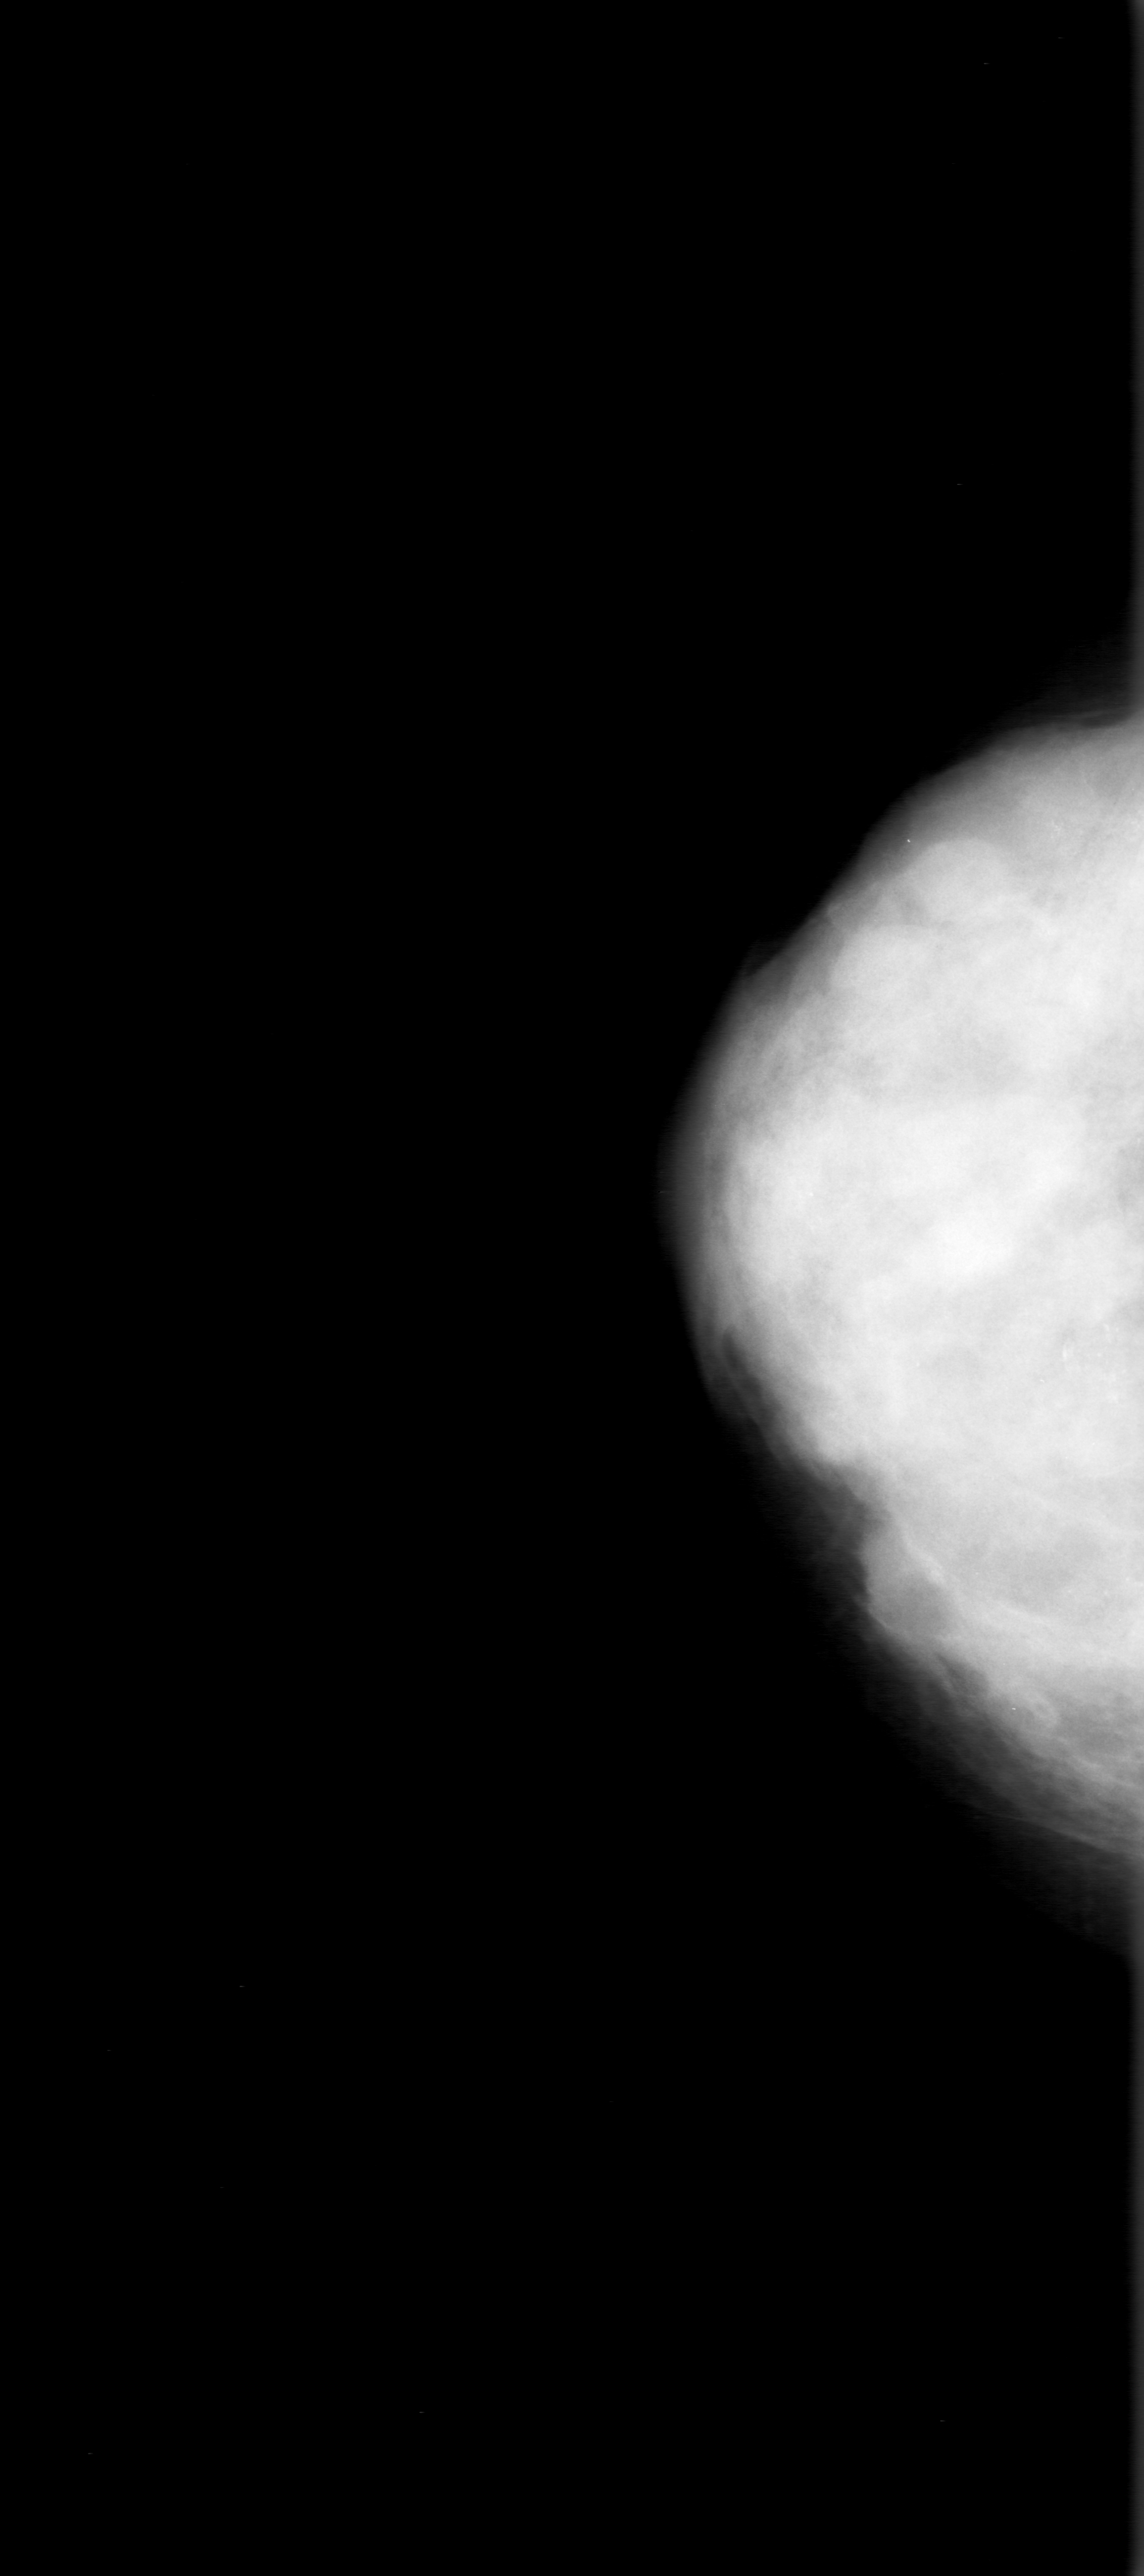
Mammogram (digitized film), right breast, craniocaudal (CC) view, breast composition: extremely dense (BI-RADS density category 4 of 4).
Marked findings (only marked abnormalities are described; nothing is implied about the rest of the image): calcifications, morphology pleomorphic, distribution segmental; BI-RADS assessment category 5; subtlety rating 5 on a 1 (subtle) to 5 (obvious) scale; pathology result (as recorded, not read from the image): malignant.